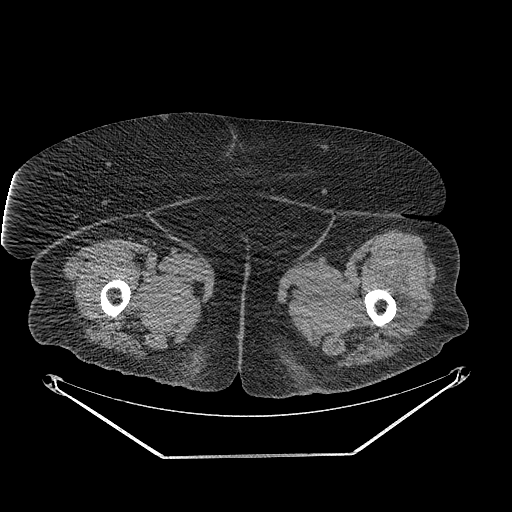
CT of an extremity soft-tissue mass (from a PET/CT study), one axial slice; slice 259 of 267 in the series (ordered by position); reconstruction kernel STANDARD; 140 kVp; soft-tissue window (W 400 / L 40 HU); 3.75 mm slice thickness; 512 × 512 image matrix, field of view 500 × 500 mm. Female patient. From the clinical record (not read from this slice): histological type: undifferentiated – high grade; grade: high; site of the primary tumour: left thigh.
Structures marked on this image (expert contour drawn on MRI and transferred to this co-registered scan by the dataset authors):
- gross tumour volume including surrounding oedema: bounding box [x1, y1, x2, y2] px = [397, 292, 417, 327]